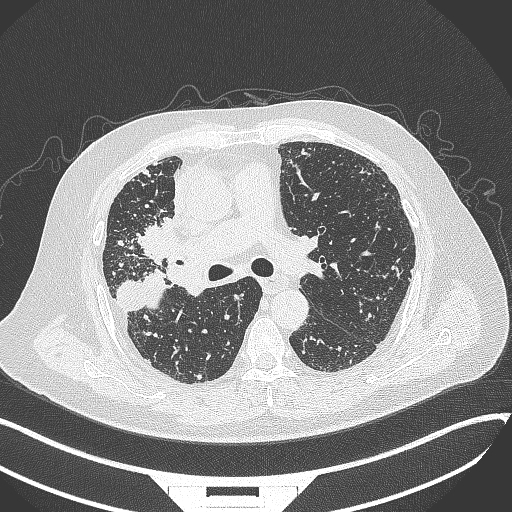
Chest CT, one axial slice. Position 209 of 384 along the scan axis. Reconstruction kernel B70f. Lung window (W 1500 / L -600 HU). 512 × 512 image matrix. Male patient, age 69 years. Case-level facts recorded for this patient, not image findings: clinical TNM (as recorded): T4 N3 M1.
Annotated regions visible in this slice (rectangle marked by the reading radiologist):
- lung tumour (recorded histology: adenocarcinoma): bounding box [x1, y1, x2, y2] px = [133, 213, 183, 267]